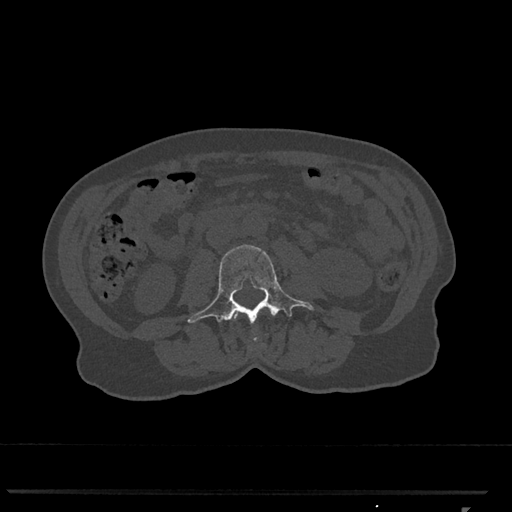
CT including the spine, one axial slice. Slice 281 of 793 in the series (ordered by position). Reconstruction kernel Br40s/3. 120 kVp. Bone window (W 1800 / L 400 HU). 512 × 512 image matrix, field of view 380 × 380 mm. Female patient, age 62 years. Case-level facts recorded for this patient, not image findings: primary cancer: renal.
Annotated regions visible in this slice (semi-automatic segmentation, software-assisted and operator-edited):
- L2 vertebra: box from (x=234, y=313) to (x=258, y=341) px
- L3 vertebra: (x=187, y=245)–(x=314, y=323)